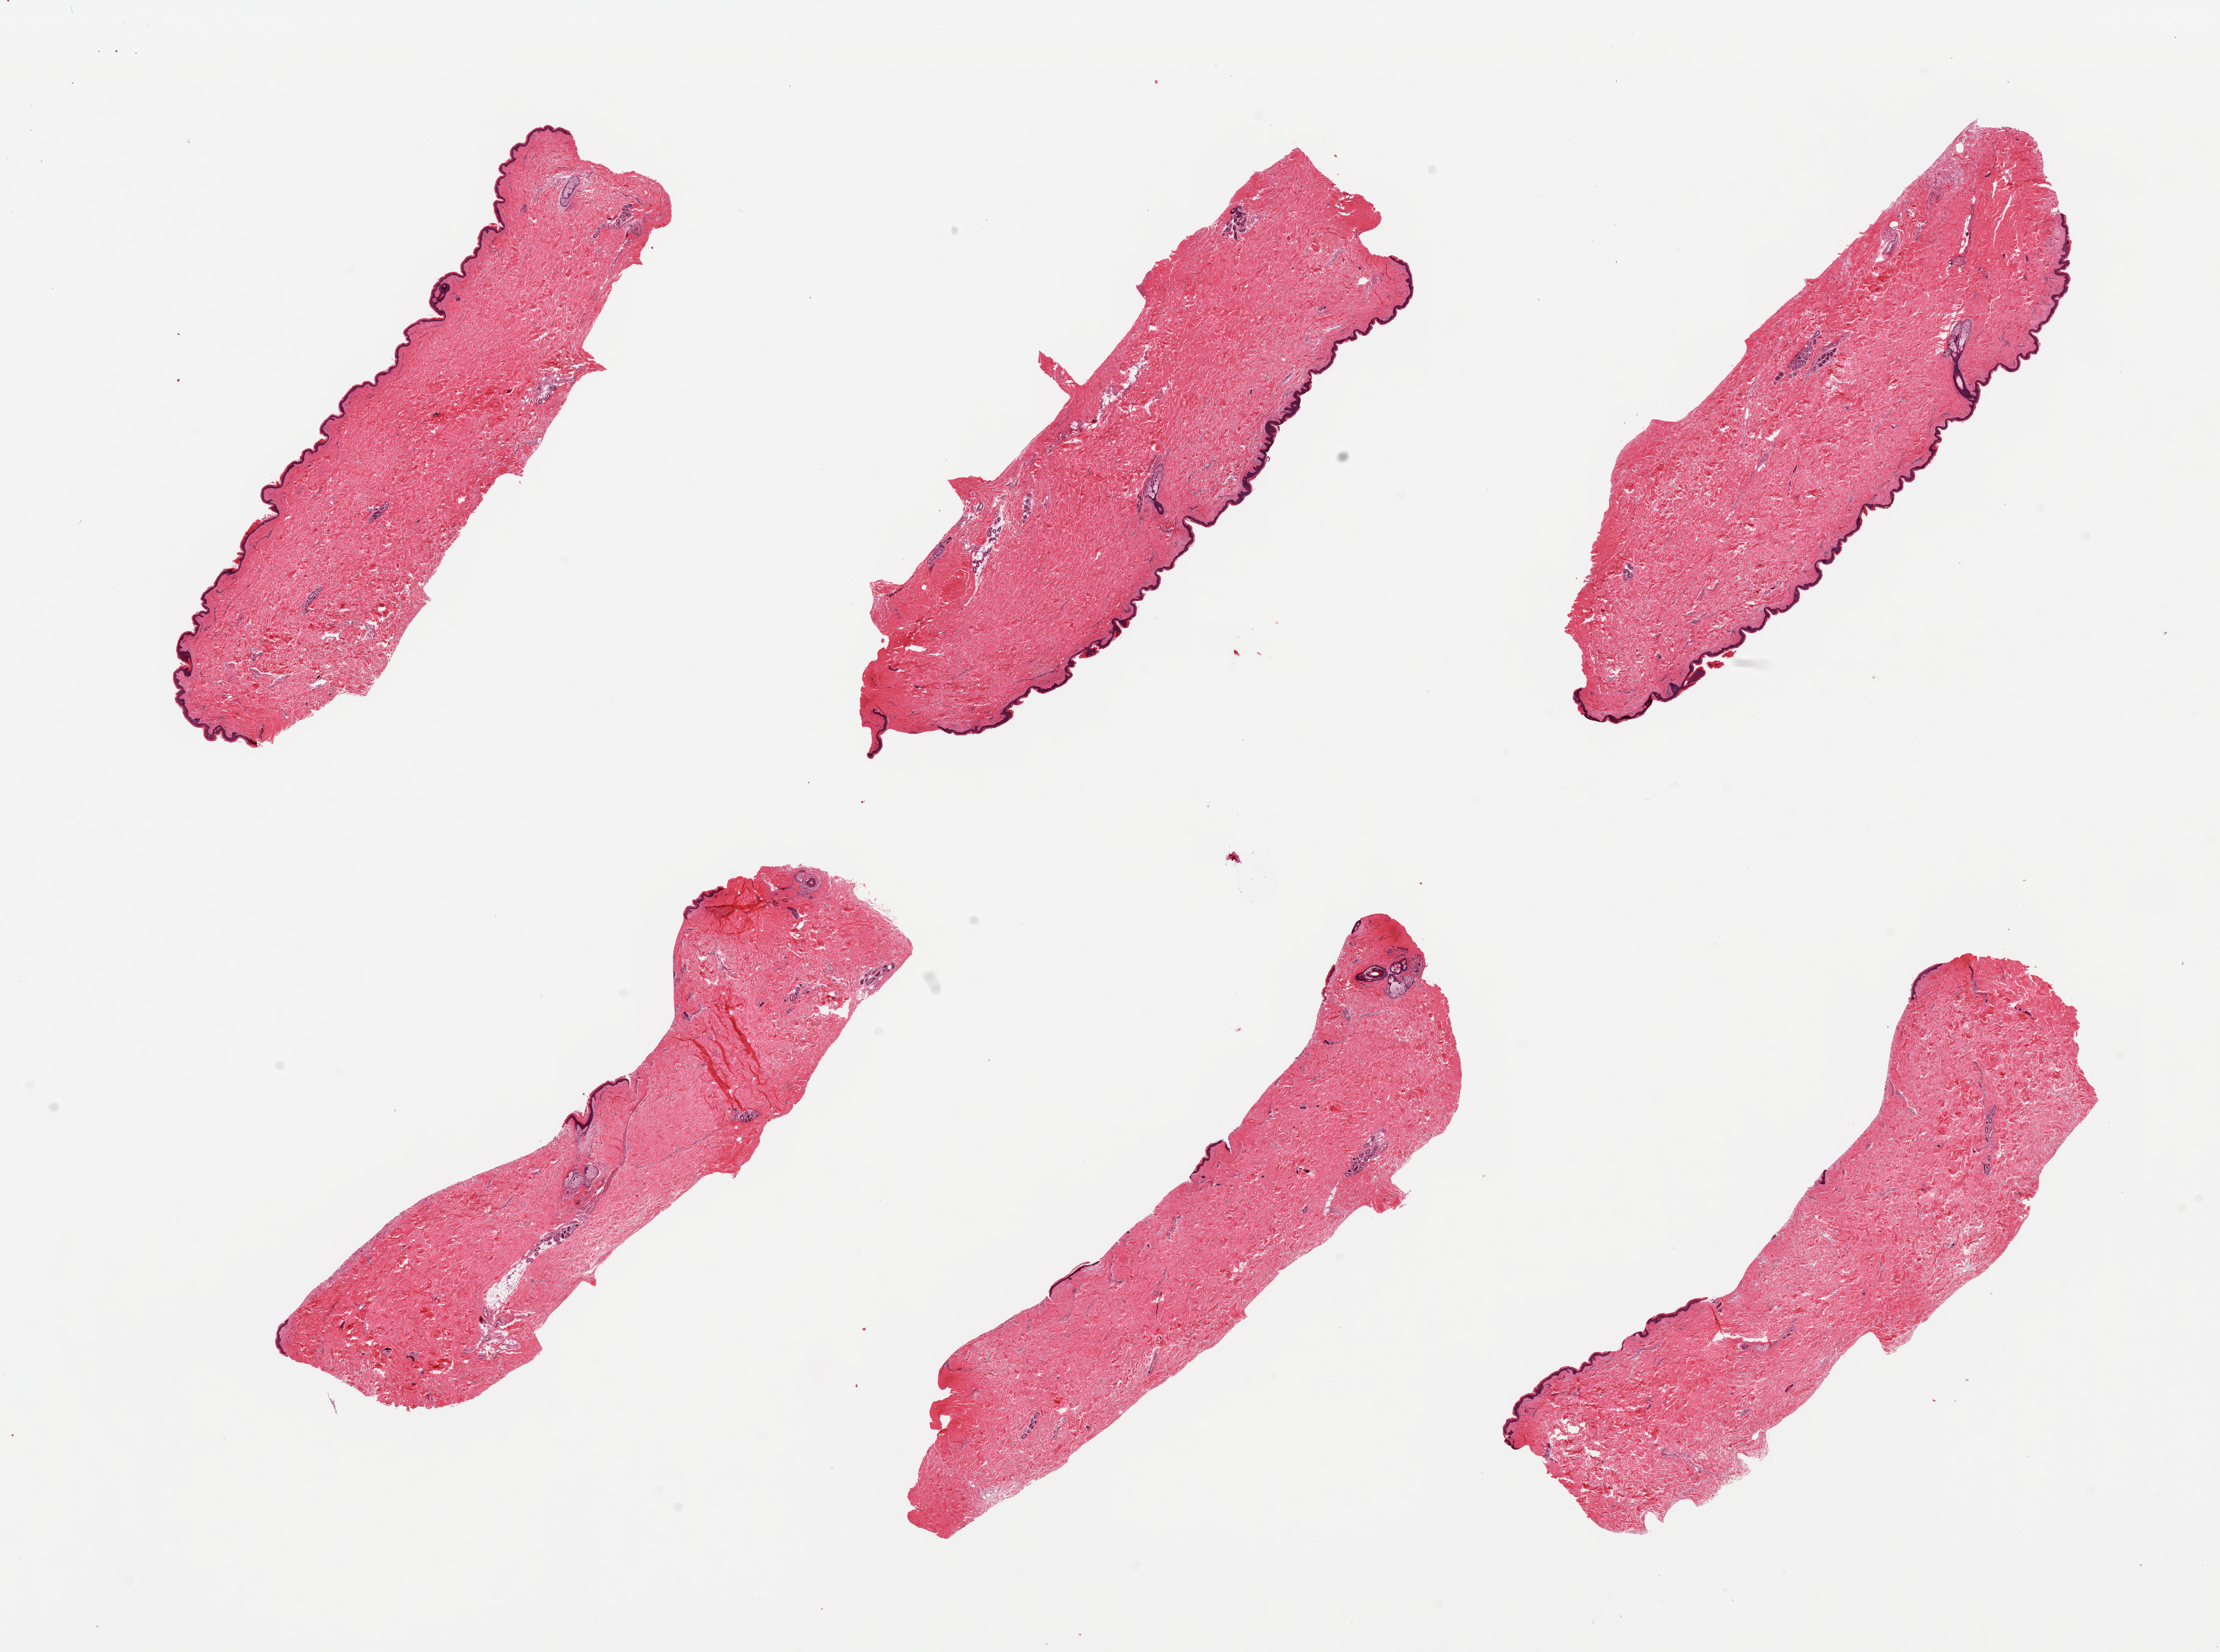
Digitized haematoxylin and eosin-stained section — shown as a low-resolution overview of the whole scanned area (about 27.6 x 20.5 mm, acquisition: 20x scan). PAXgene-fixed paraffin-embedded (PFPE) section. Sampled site (target tissue): skin of suprapubic region. Tissue donor sample. Male donor.
Reviewer comment on this tissue sample: 6 pieces; well trimmed, very minimal internal fat.